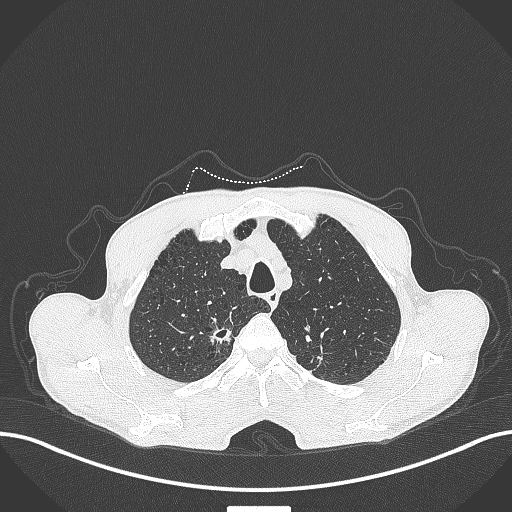
Chest CT, one axial slice. Position 358 of 445 along the scan axis. 120 kVp. Lung window (W 1500 / L -600 HU). 512 × 512 image matrix, field of view 400 × 400 mm. Patient: male, 70 years. From the clinical record (not read from this slice): clinical TNM (as recorded): T1a N0 M0.
Structures marked on this image (bounding box drawn by a radiologist):
- lung tumour (recorded histology: adenocarcinoma): bounding box (x1, y1, x2, y2) in pixels: (207, 318, 236, 348)